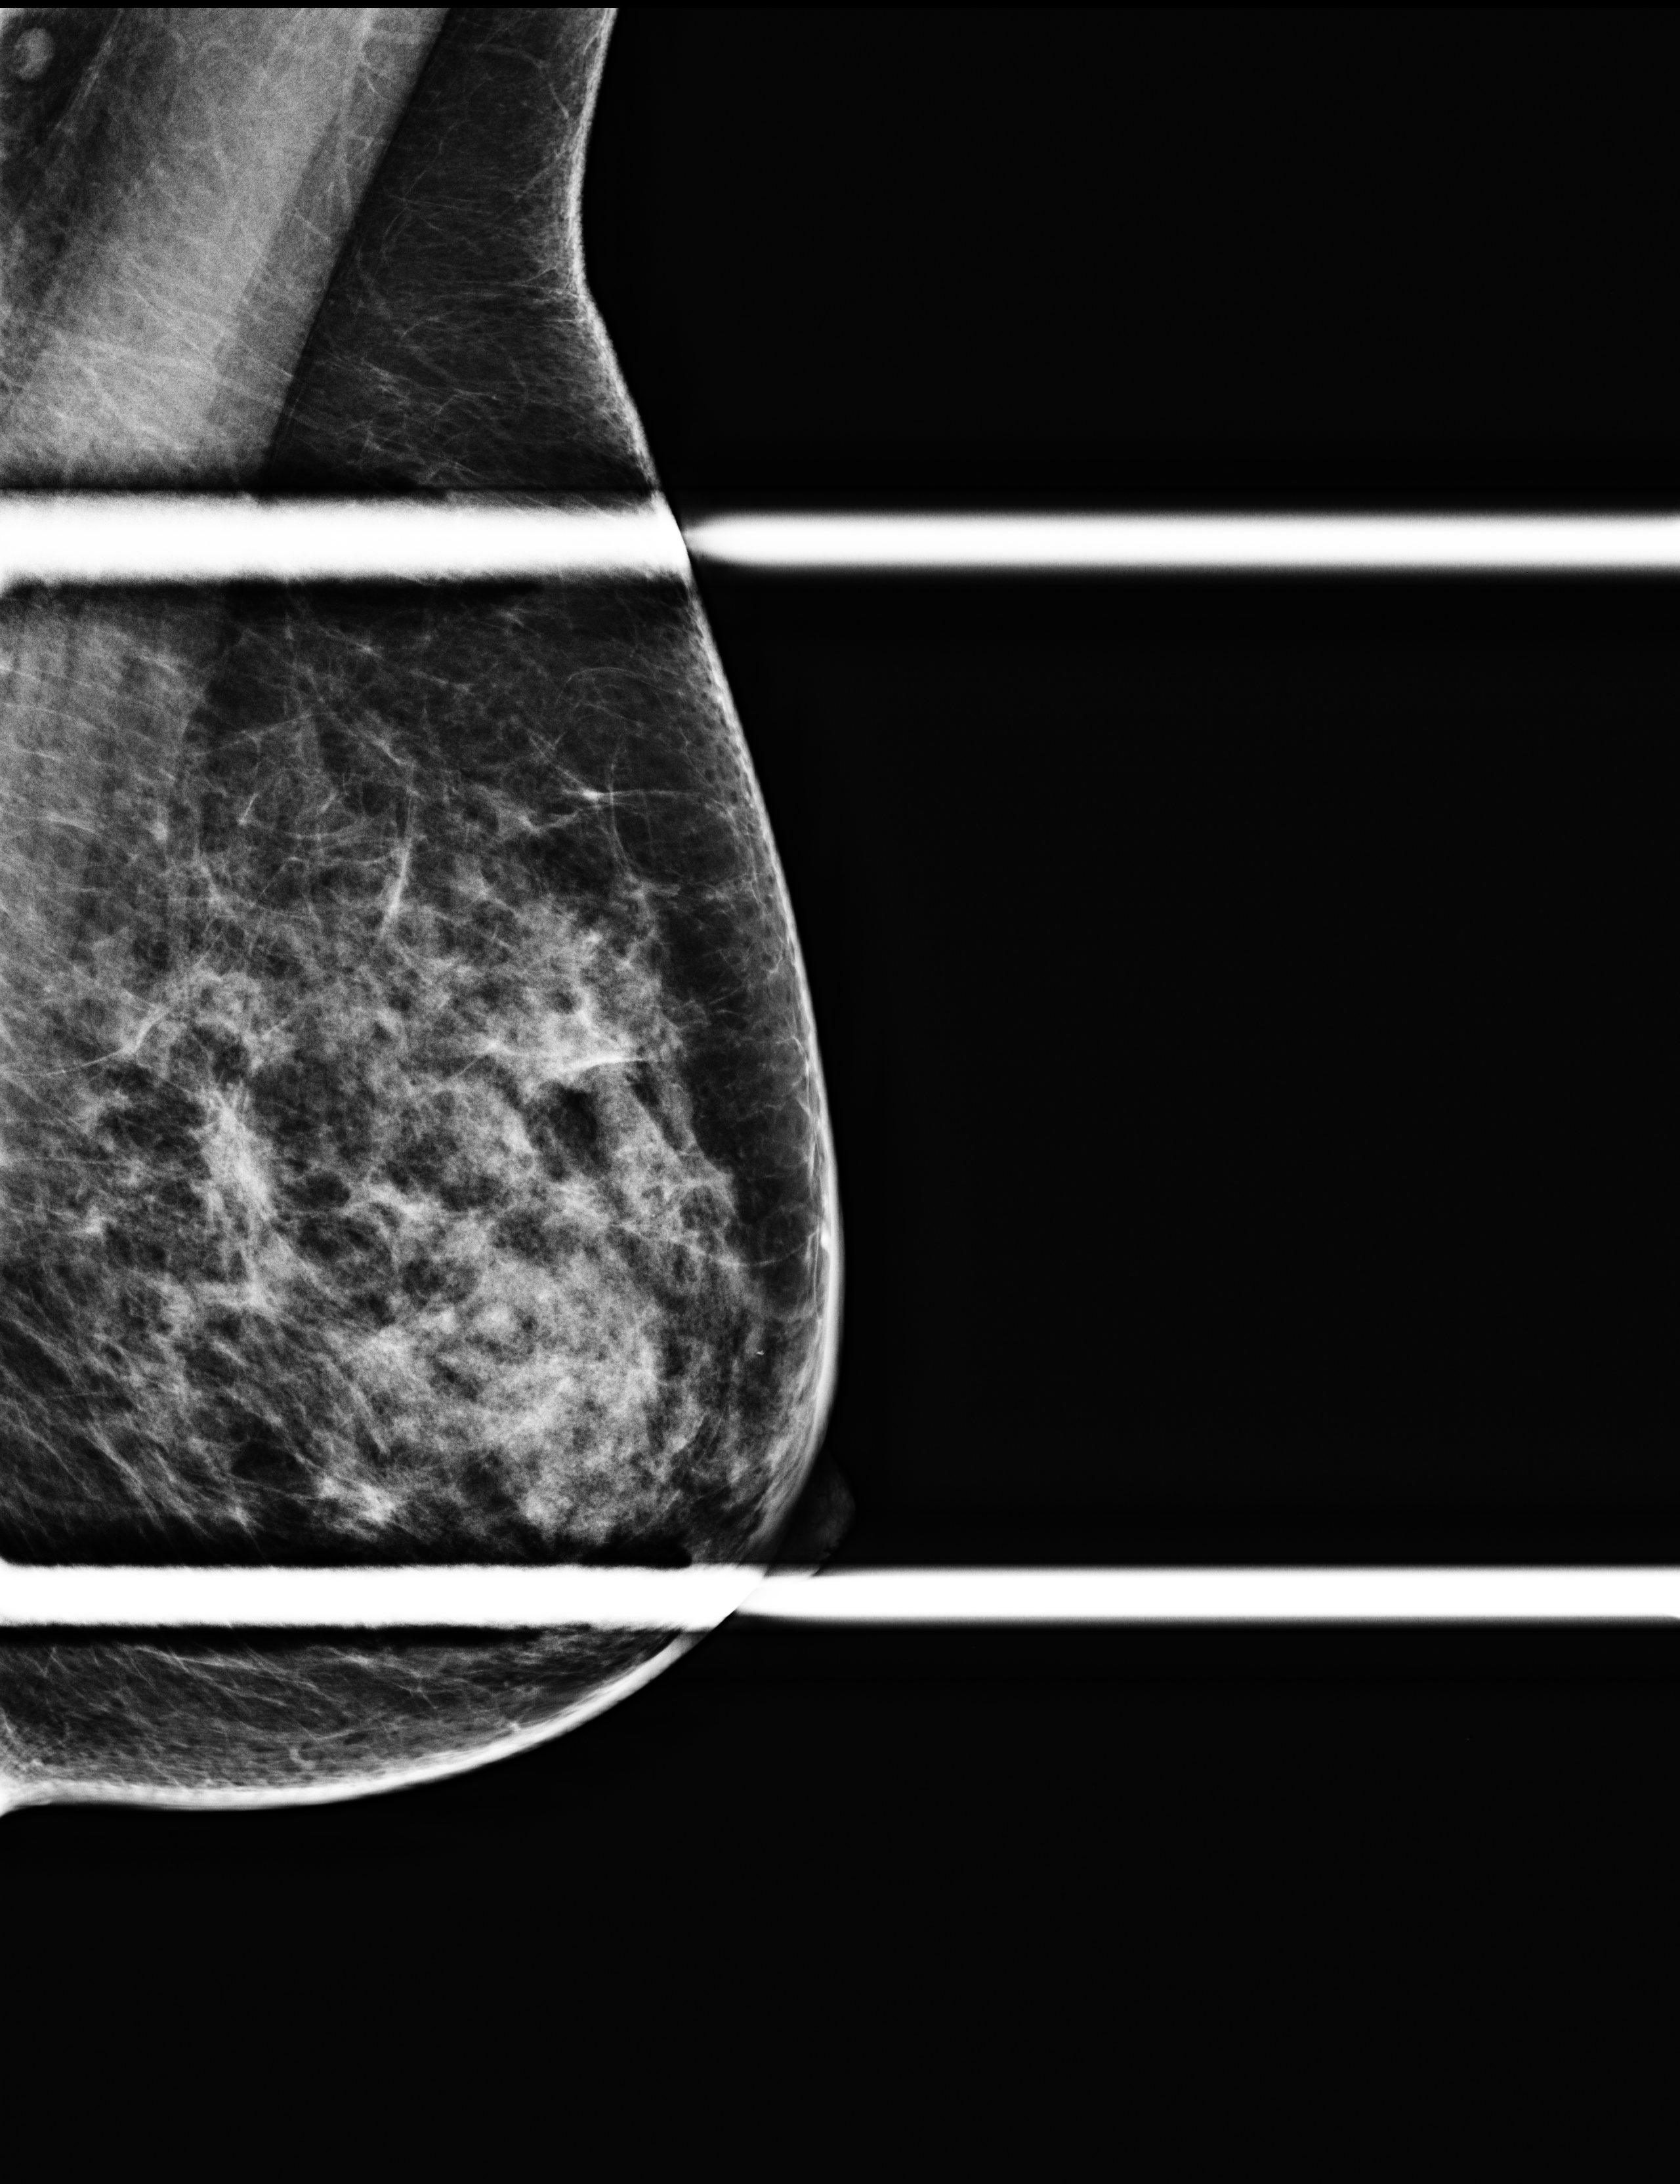
Digital mammogram (FFDM); left breast; mediolateral oblique (MLO) view (spot compression); annual screening mammography examination. Female patient, age 61 years.
- BI-RADS breast density category at the screening exam (both breasts, scale 1–4): 3
- final BI-RADS category for the screening round (tomosynthesis exam, both breasts): category 1
- recall: no recall after this screen